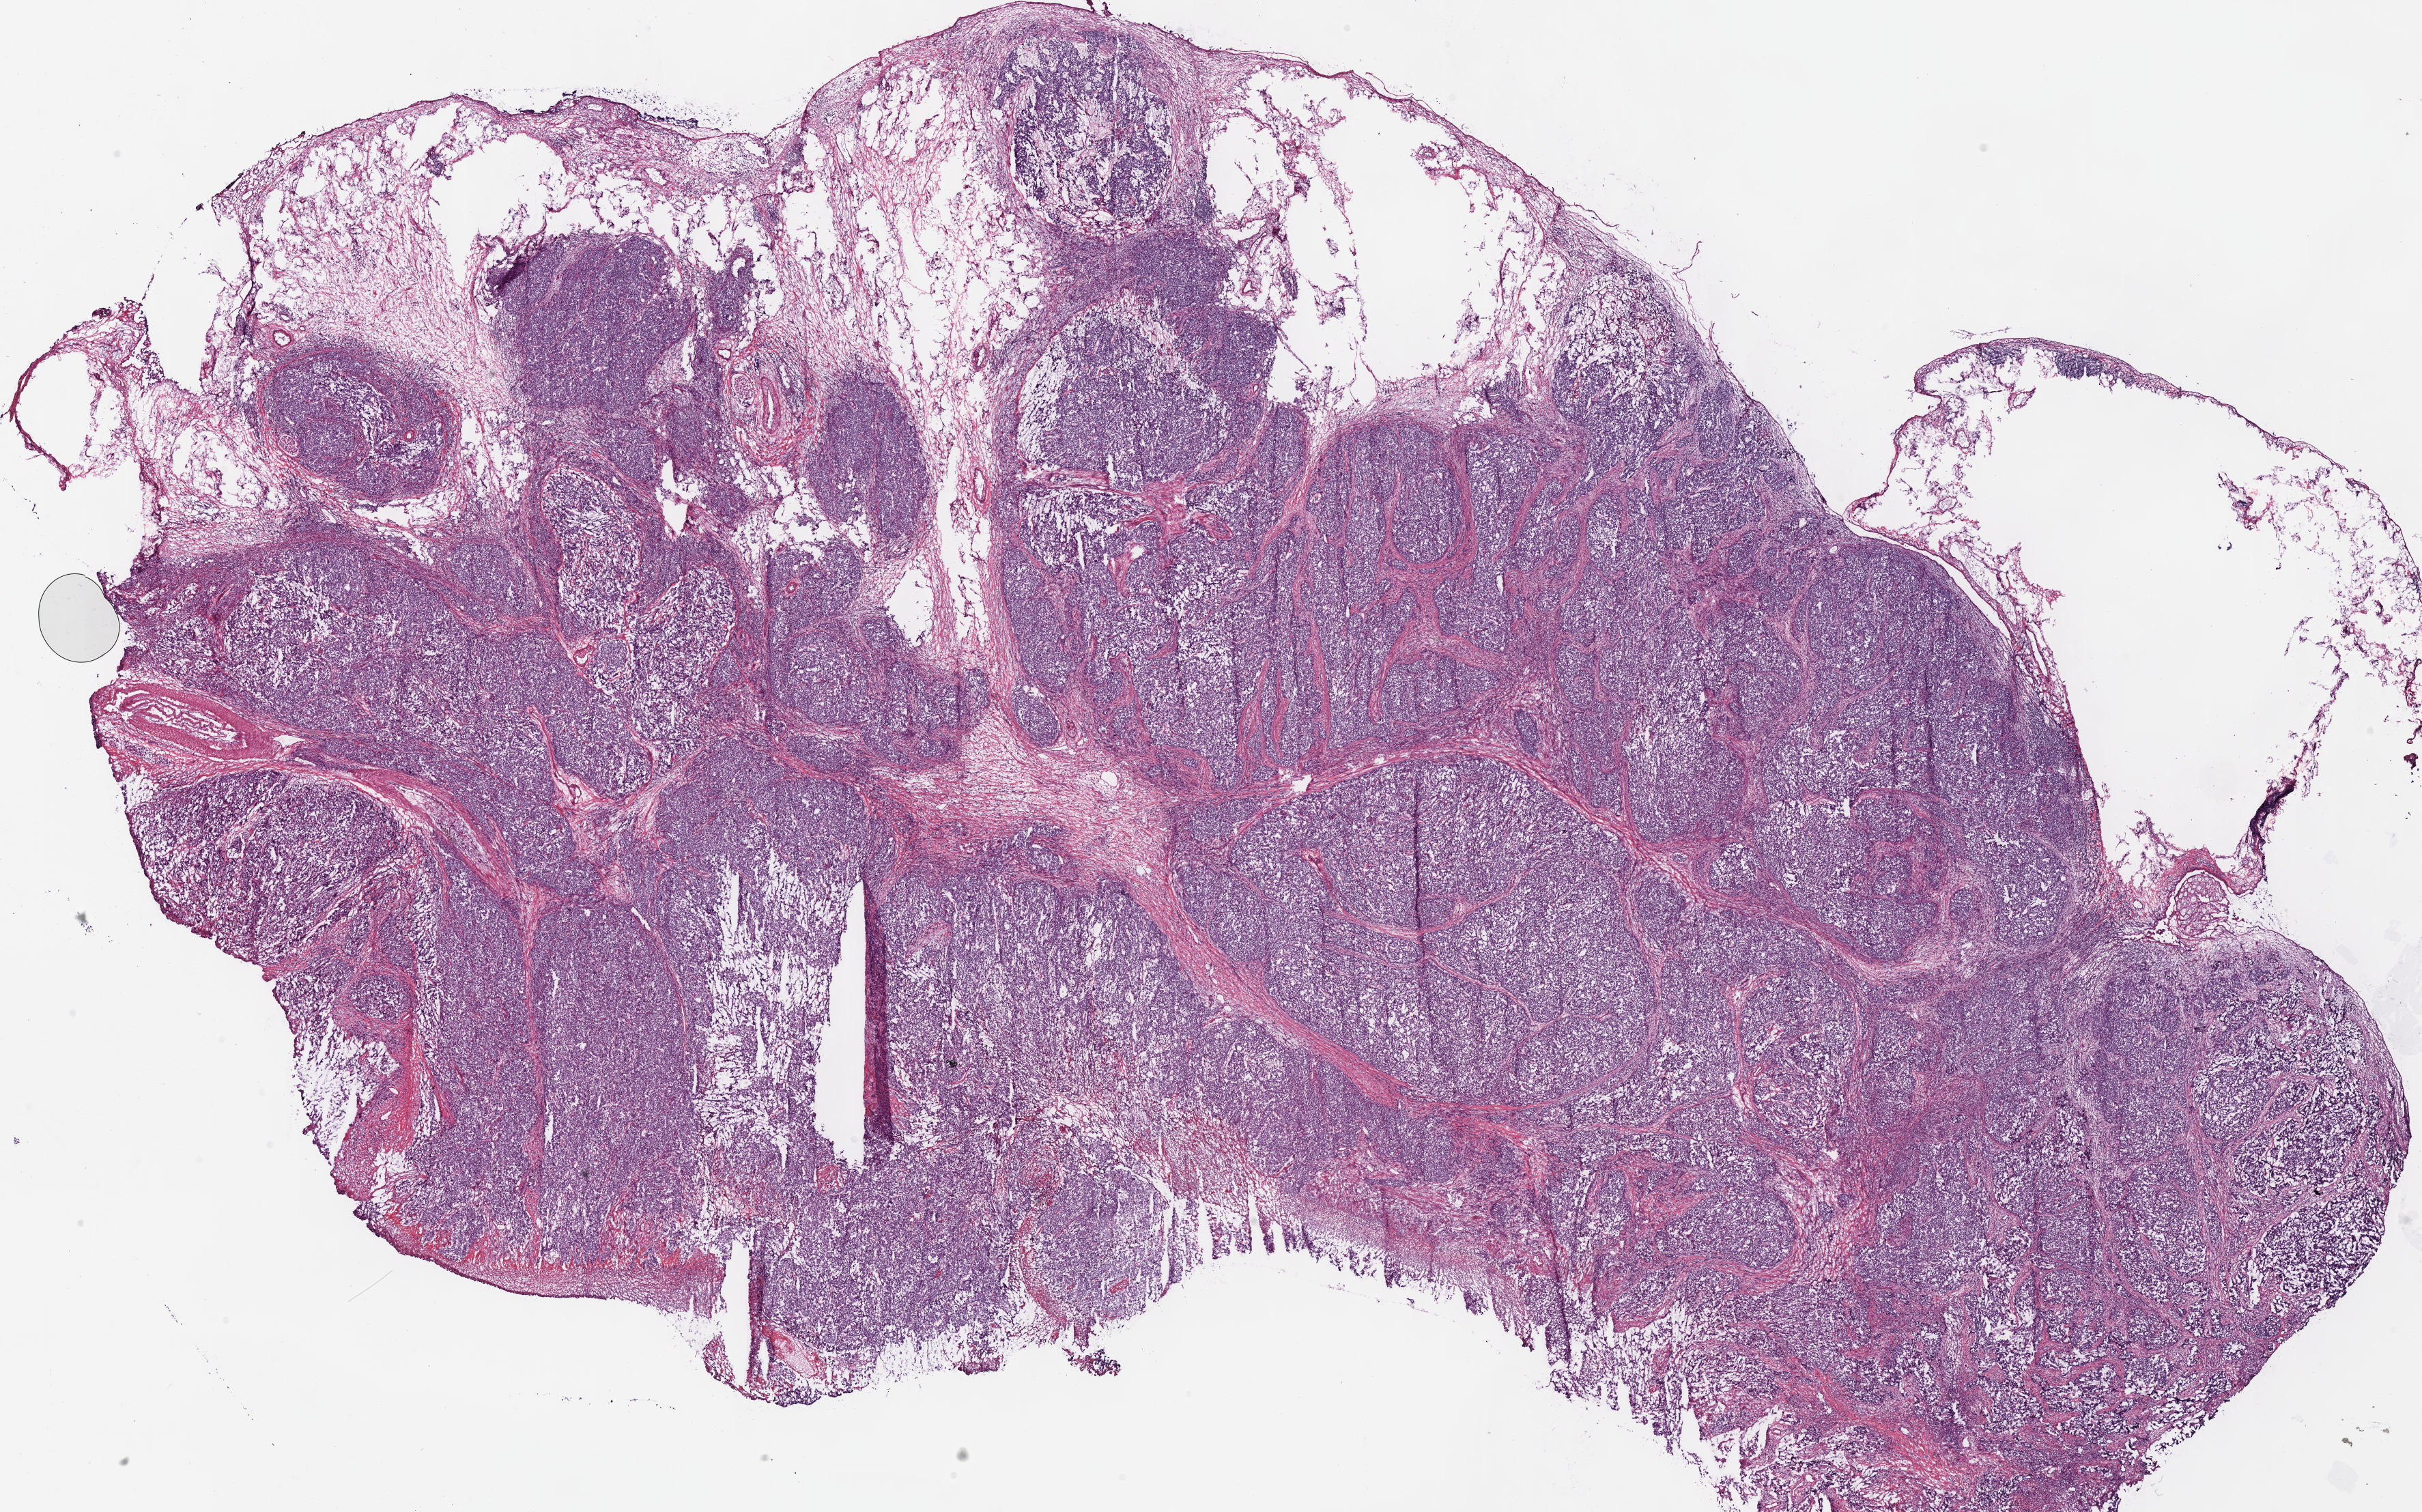
H&E-stained whole-slide image — a low-resolution overview of the entire scanned area, about 27.9 x 17.4 mm; frozen section from the bottom of the tissue portion; sample: primary tumour, stomach. Patient: male, age at initial diagnosis 59 years. Histologic grade: G3 (poorly differentiated). Composition of this section per pathologist review: tumour cells 90%, tumour nuclei 85%, normal cells 0%, stromal cells 10%, necrosis 0%. Inflammatory infiltration, as recorded: lymphocyte infiltration 10%, monocyte infiltration 0%, neutrophil infiltration 0%.
* histologic diagnosis: Adenocarcinoma, NOS (body of stomach)
* AJCC pathologic stage: IIIB (7th edition)